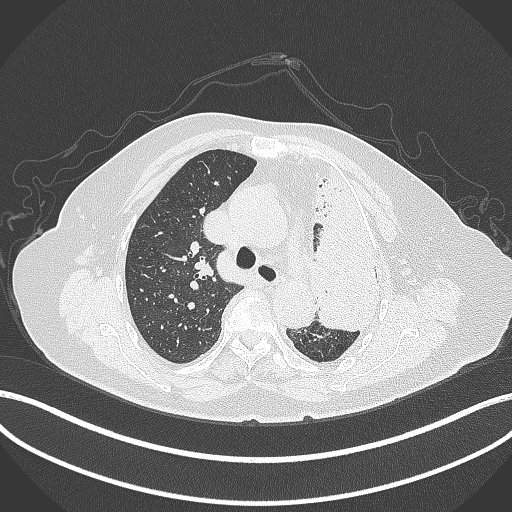
Chest CT, one axial slice. Slice 277 of 399 in the series (ordered by position). Lung window (W 1500 / L -600 HU). 512 × 512 image matrix, field of view 400 × 400 mm. Patient: female, 75 years. From the clinical record (not read from this slice): clinical TNM (as recorded): T3 N3 M1.
Annotated regions visible in this slice (bounding box drawn by a radiologist):
- lung tumour (recorded histology: adenocarcinoma): bounding box [x1, y1, x2, y2] px = [308, 157, 387, 334]